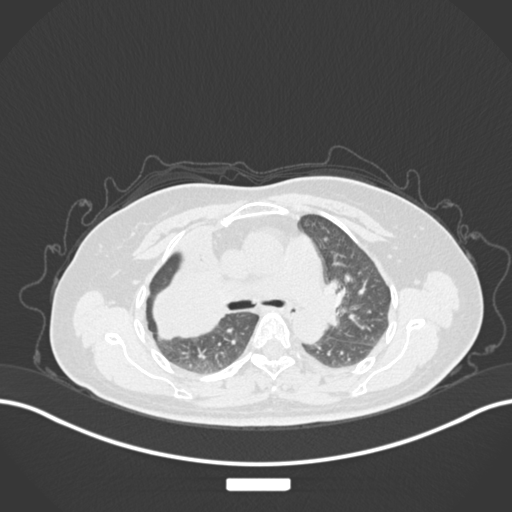
Chest CT, one axial slice. Position 99 of 177 along the scan axis. 120 kVp. Lung window (W 1500 / L -600 HU). 512 × 512 image matrix. Patient: female, 60 years. From the clinical record (not read from this slice): clinical TNM (as recorded): T3 N1 M1.
Structures marked on this image (bounding box drawn by a radiologist):
- lung tumour (recorded histology: adenocarcinoma): bounding box [x1, y1, x2, y2] px = [151, 243, 229, 349]